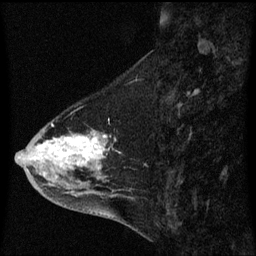
Breast MRI (dynamic contrast-enhanced), one sagittal slice; slice 23 of 60 in the series (ordered by position); dynamic contrast-enhanced series, image 2 of 3 at this slice position (ordered by acquisition); 1.5 T; TE 4.2 ms, TR 8.4 ms; 2 mm slice thickness; 256 × 256 image matrix. Female patient, age 46 years. Case-level facts recorded for this patient, not image findings: setting: breast cancer imaged before/during neoadjuvant chemotherapy; receptor status: HER2-positive.
Structures marked on this image (semi-automatic segmentation, software-assisted and operator-edited):
- analysis volume of interest (the breast-tissue region the enhancement analysis was run in; not a lesion): bounding box [x1, y1, x2, y2] px = [18, 118, 121, 195]
- tumour enhancement mask (voxels above the 70 % enhancement threshold inside the analysis volume of interest): [51, 136, 108, 165]